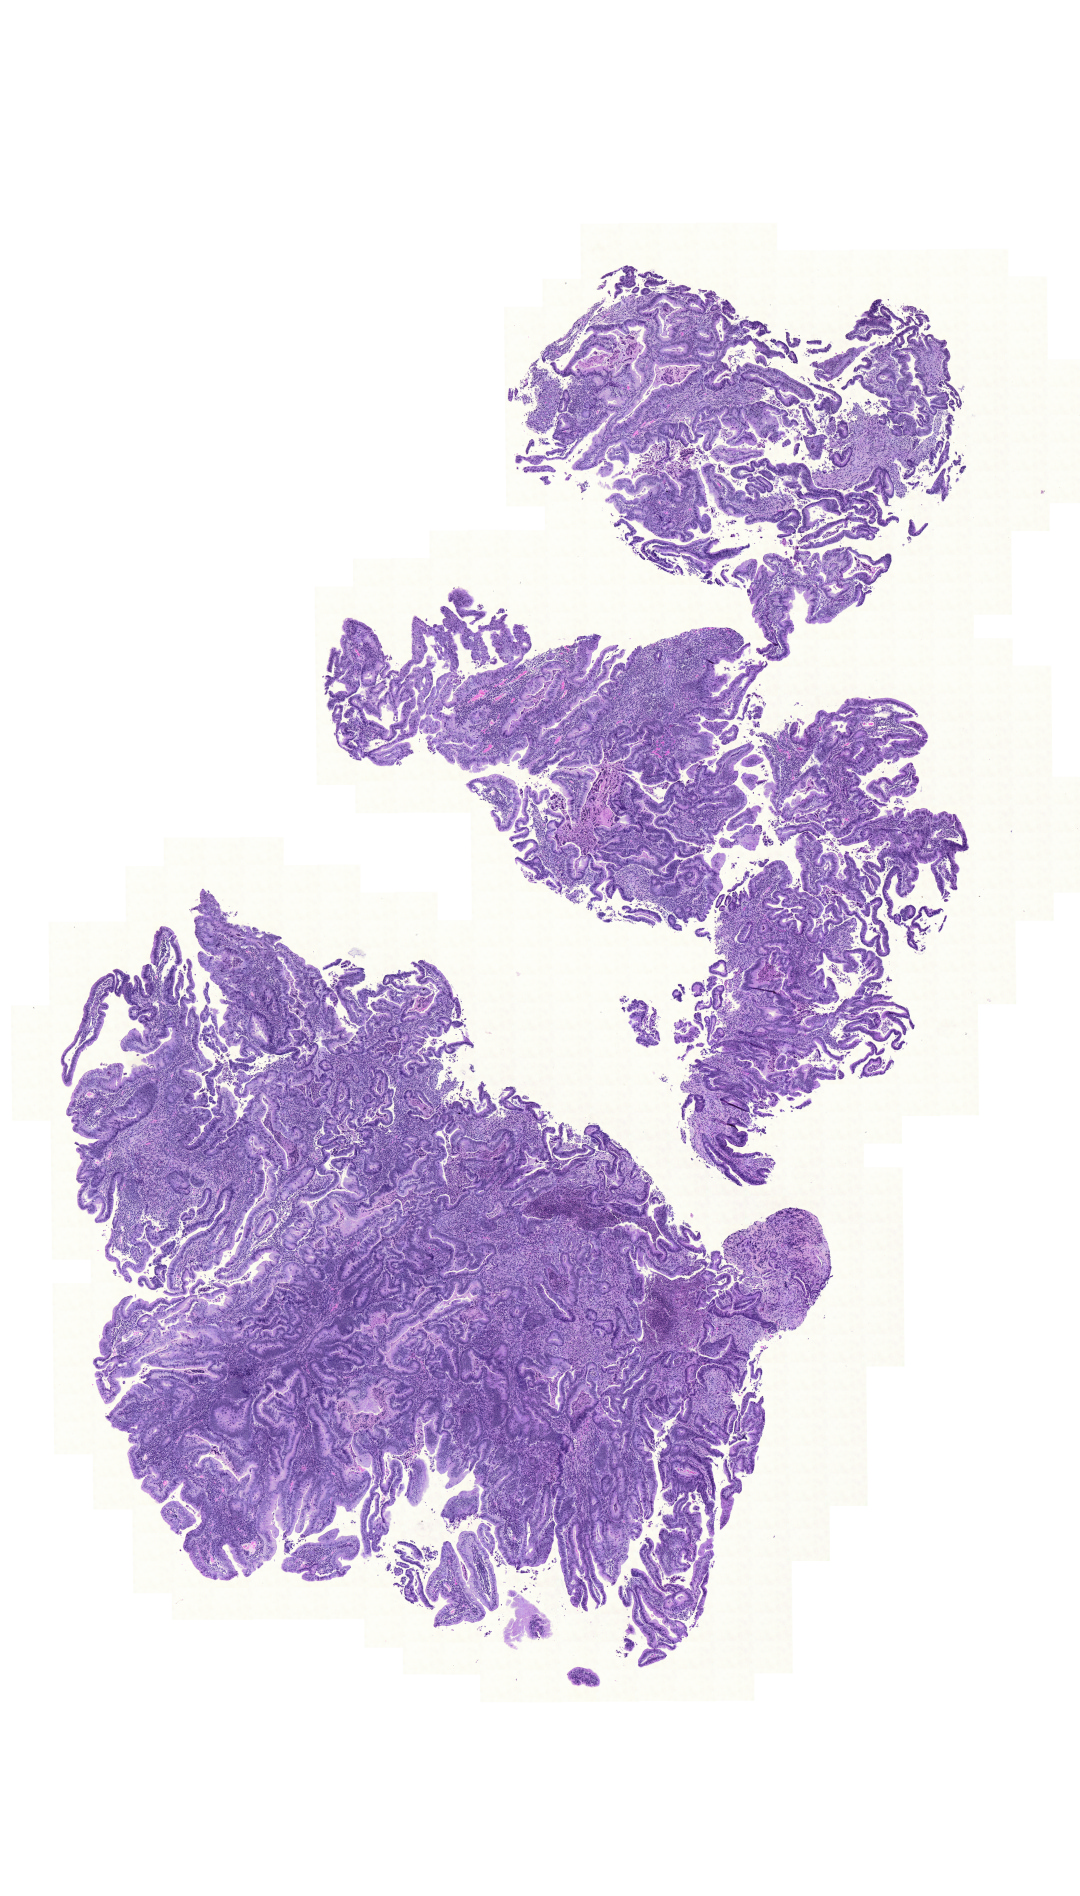
Whole-slide histology image, Hematoxylin and eosin (H&E) stained, low-resolution overview of the scanned area, about 8.0 x 14.1 mm, formalin-fixed paraffin-embedded (FFPE) diagnostic section, colon, primary tumour sample. Female, age 74 years at initial diagnosis.
AJCC pathologic stage: IIIC. Pathologic diagnosis: Adenocarcinoma, NOS (sigmoid colon). Lymph nodes positive (case pathology): 4 of 35 examined.